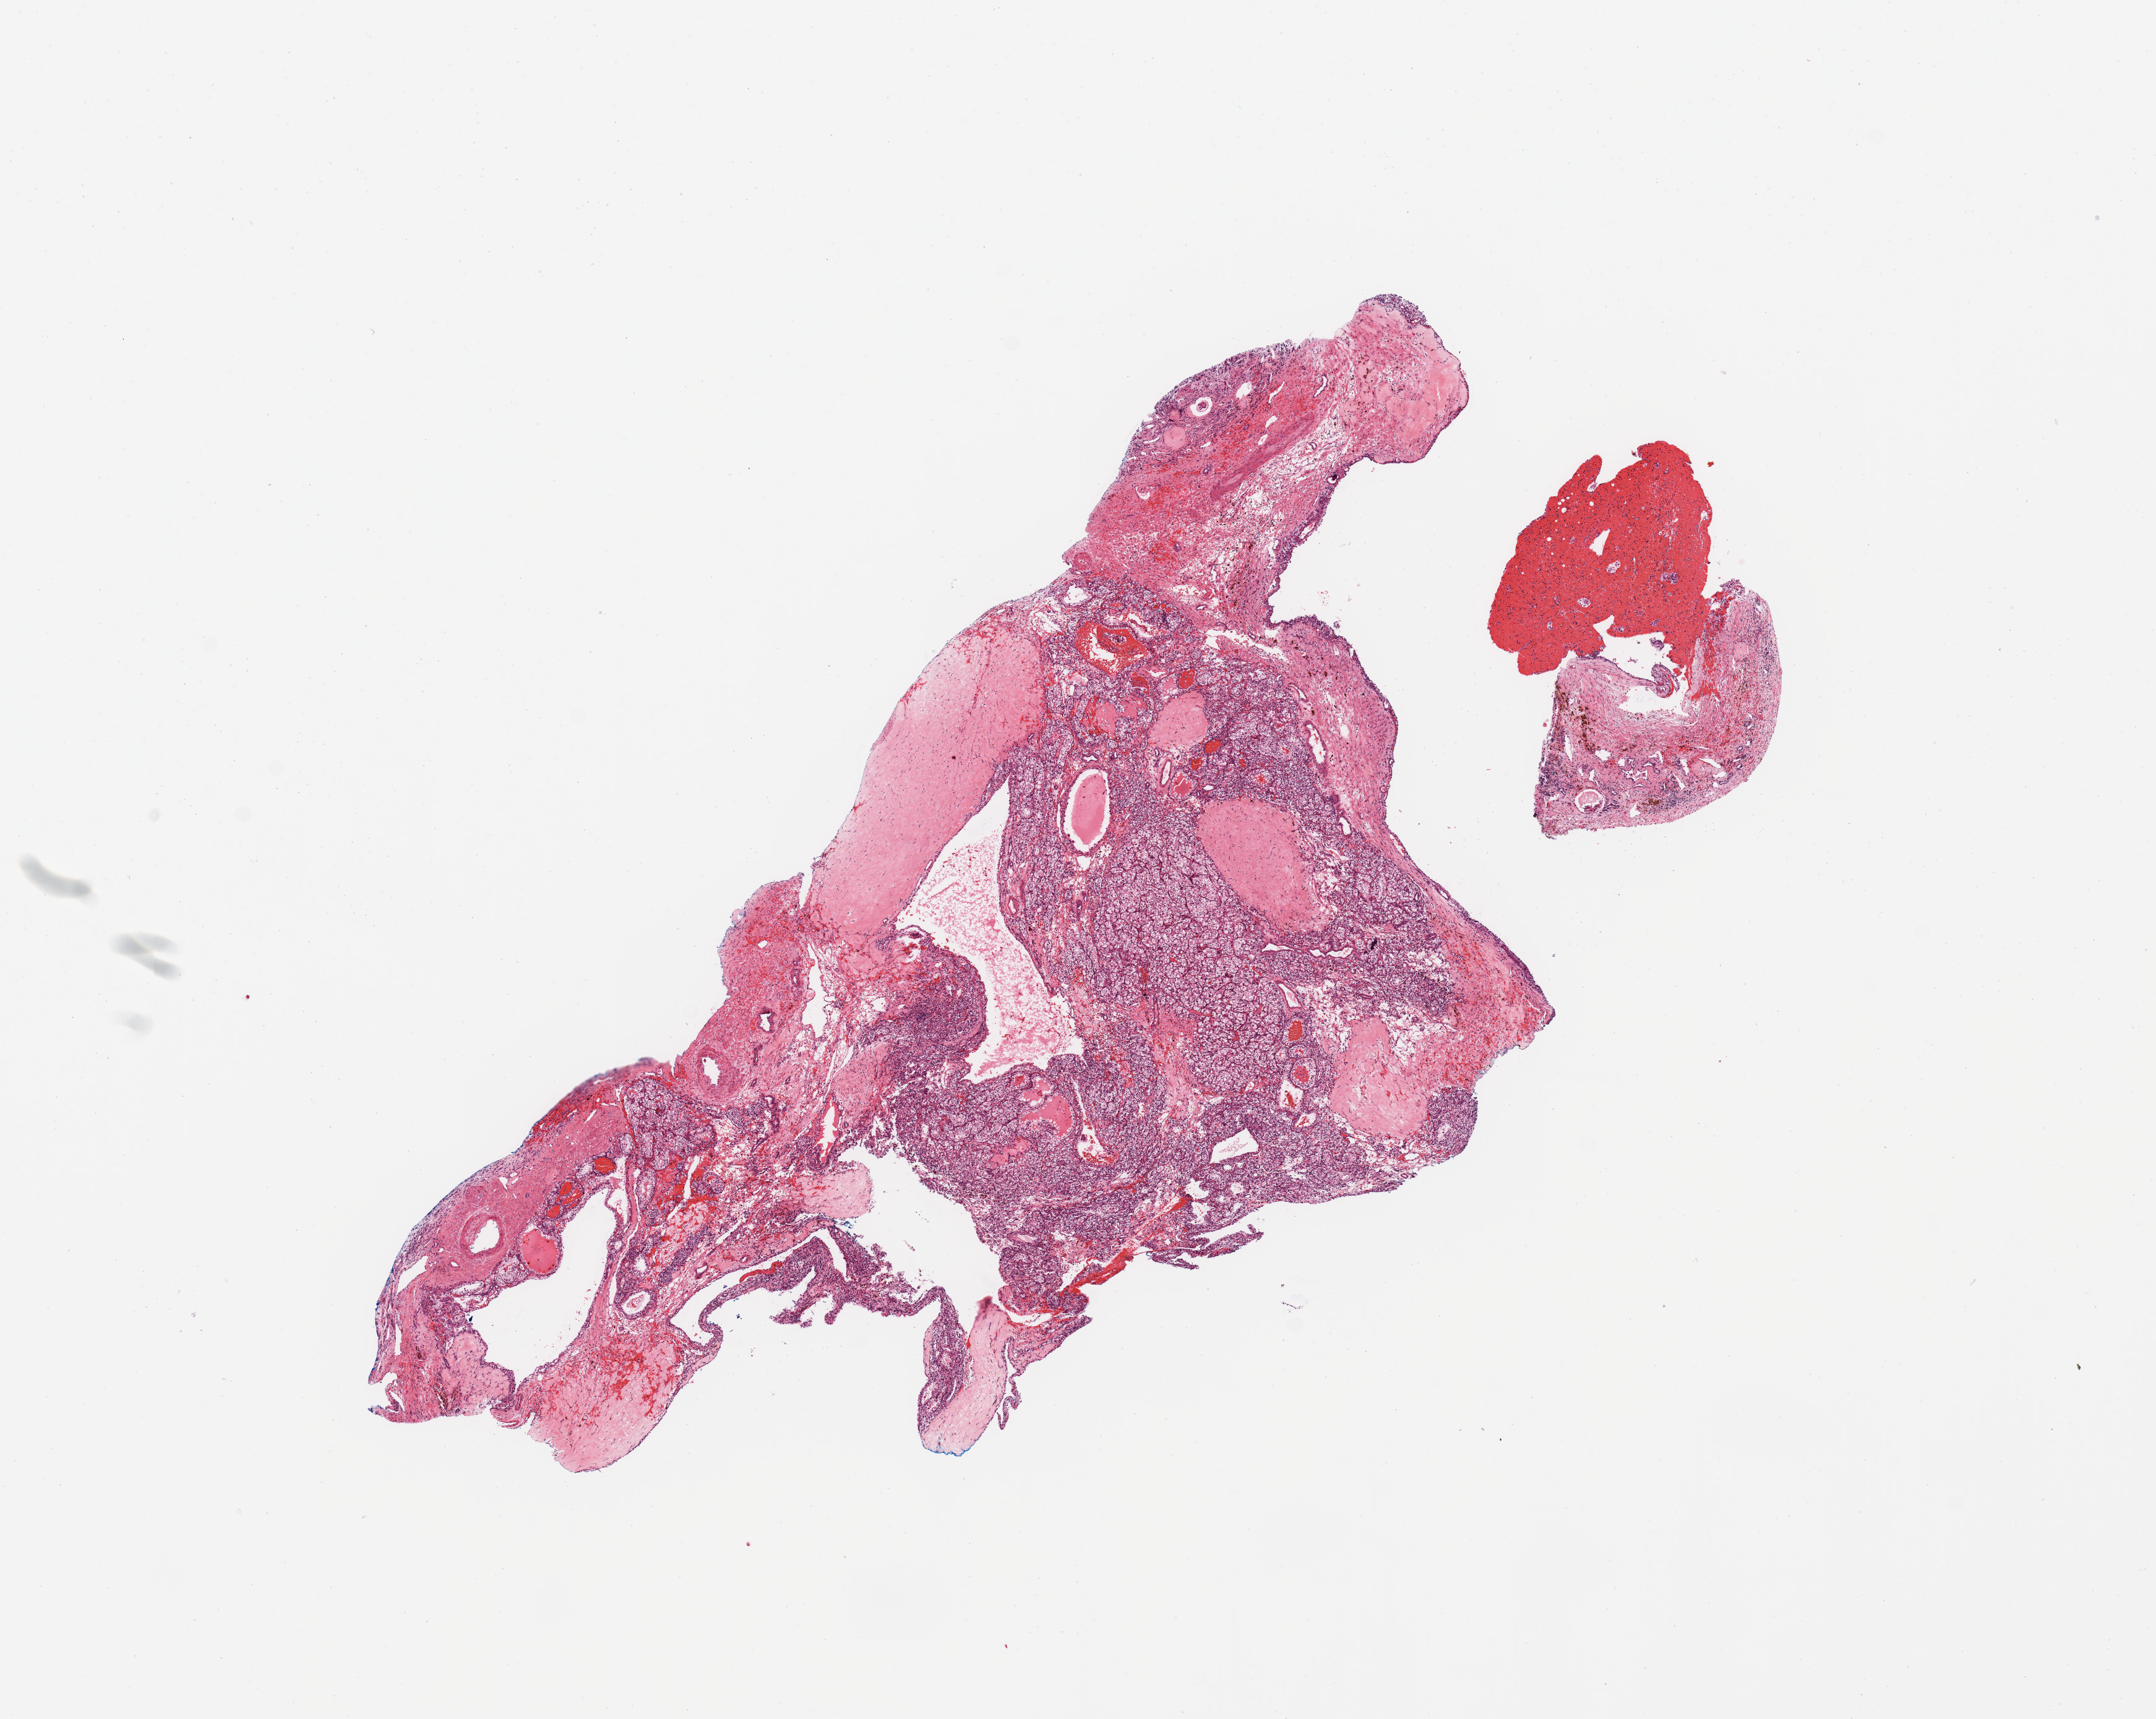
Hematoxylin and eosin (H&E) stained whole-slide image, low-resolution overview of the scanned area, about 13.8 x 11.0 mm (slide scanned at 20x). Kidney, tumour tissue. Male, 56 y/o.
Histologic diagnosis: Renal cell carcinoma, NOS.